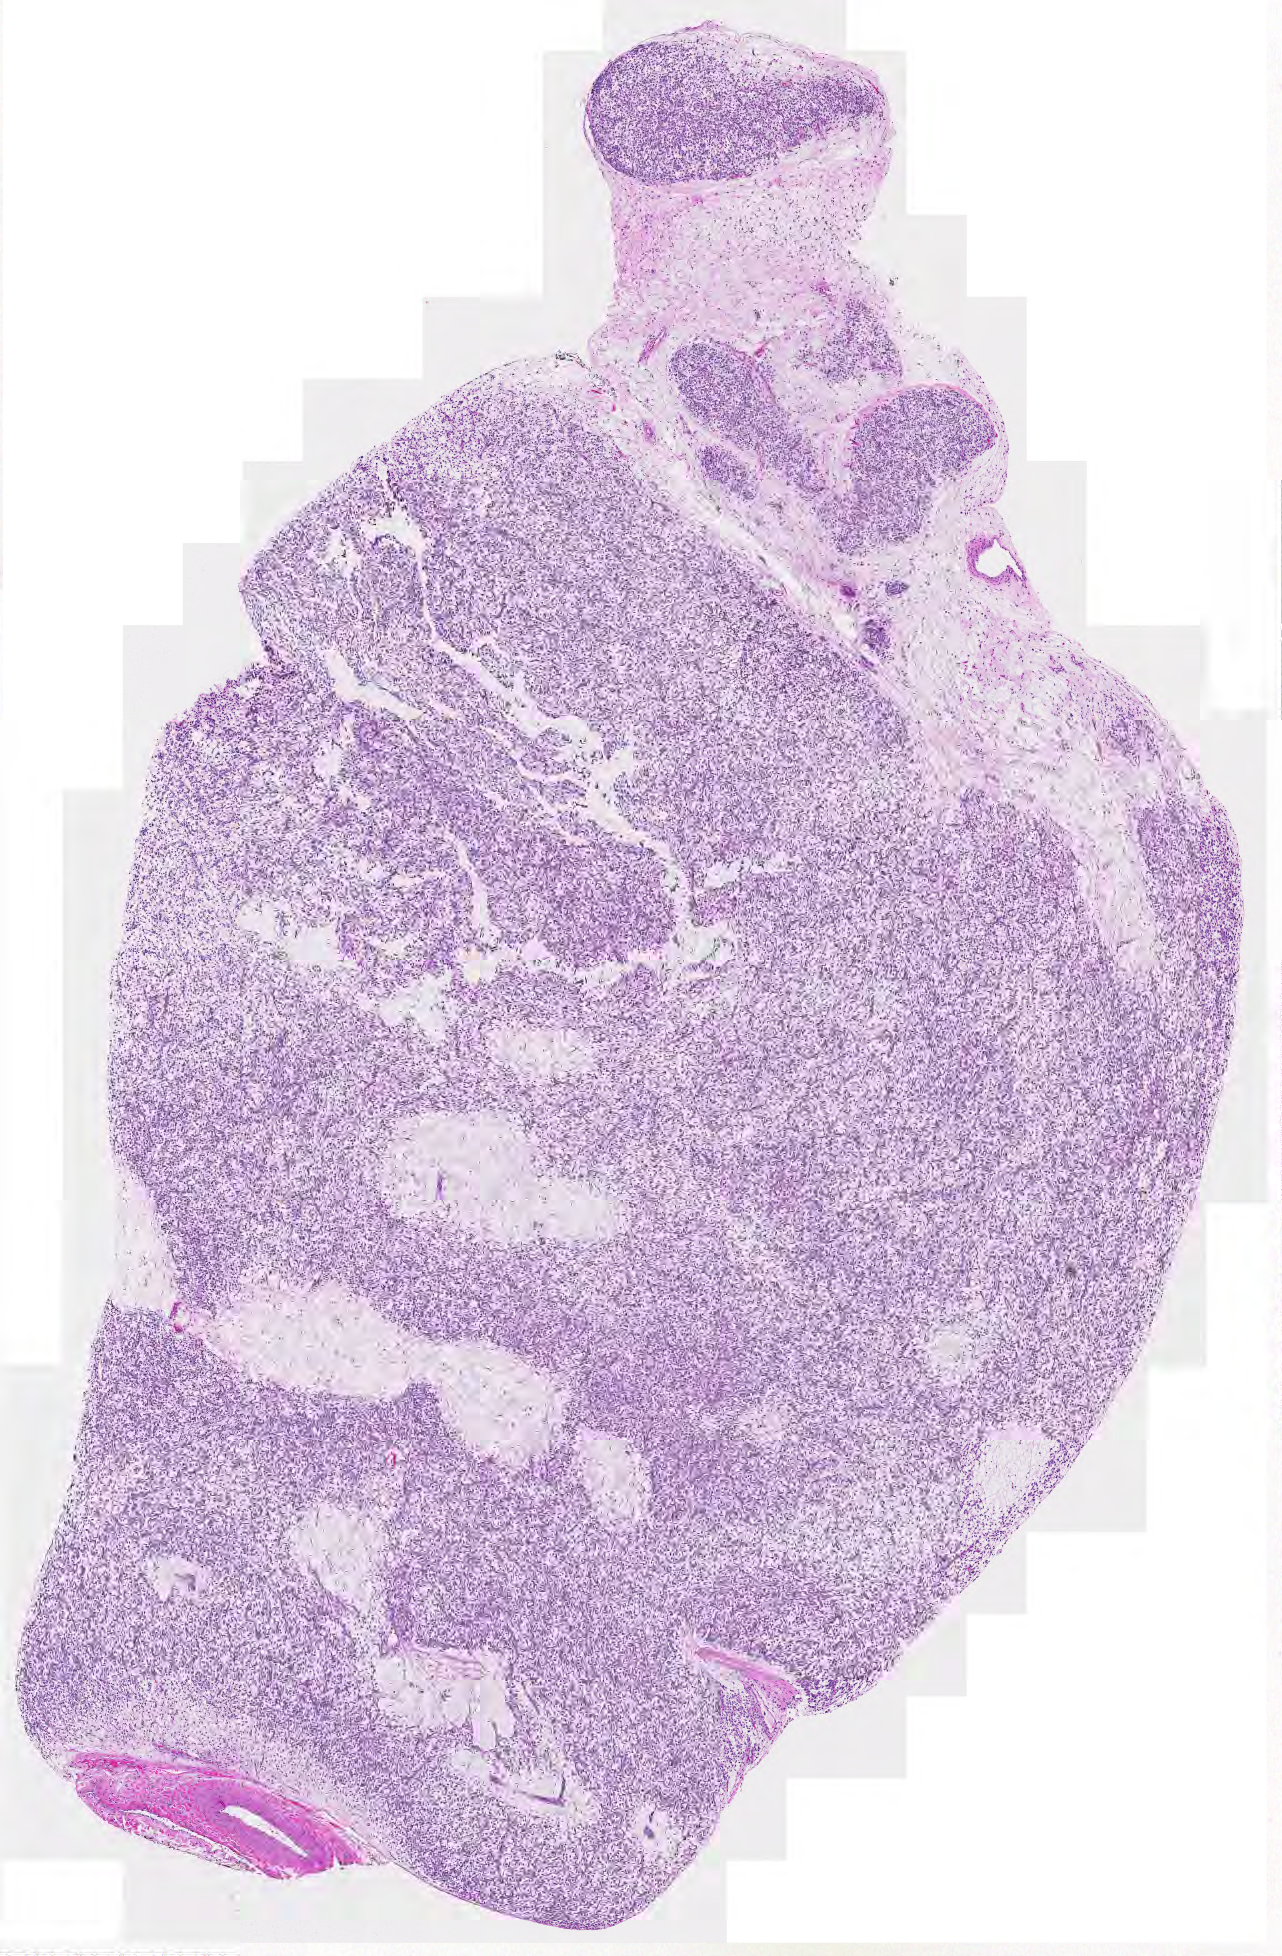
Whole-slide histology image, H&E-stained — whole scanned area (about 6.6 x 10.1 mm, slide scanned at 20x) shown as a low-resolution overview. Tumour tissue sample. Female, 41 y/o.
Primary tumour site (as recorded): lower extremity. Patient diagnosis (cohort enrolment): sarcoma (site not recorded at cohort level).